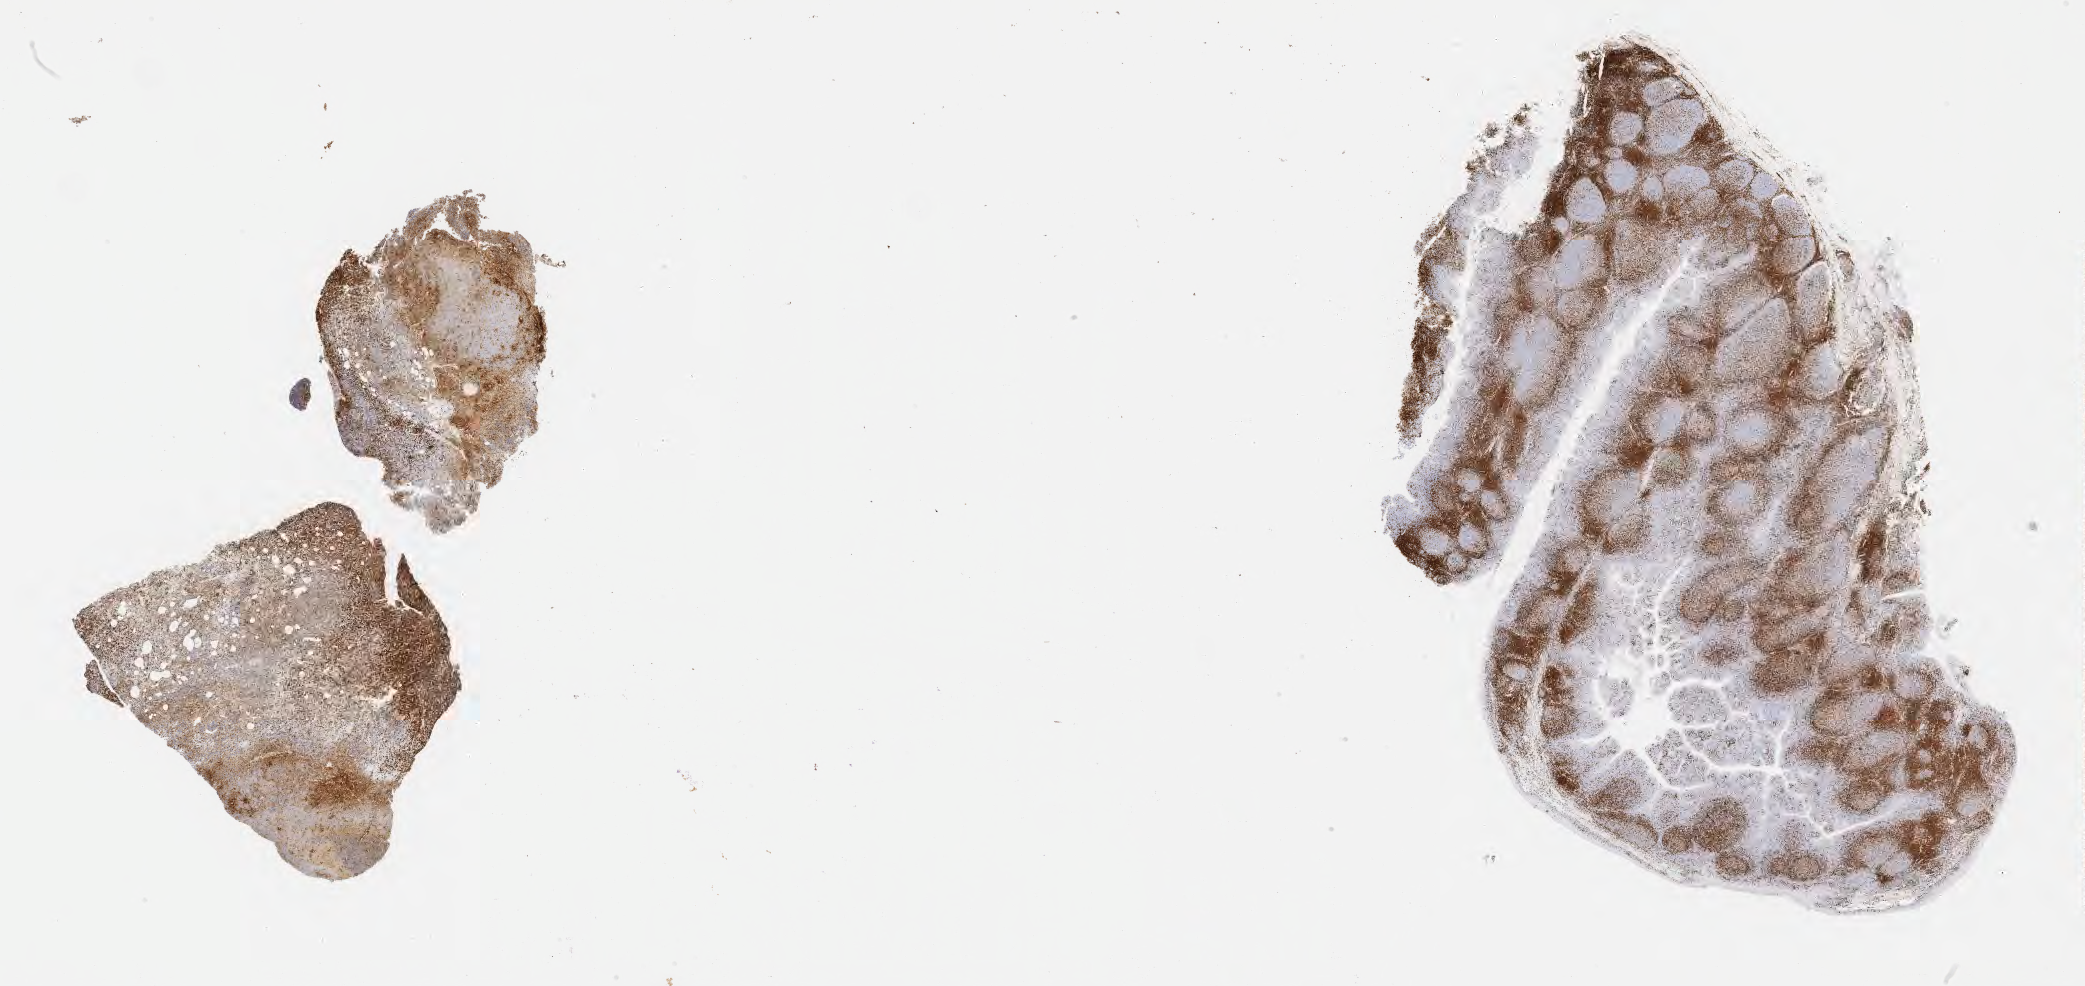
Immunohistochemistry (IHC) whole-slide image stained for CD3 — low-resolution overview of the scanned area, about 33.7 x 15.9 mm. Tumor tissue. Site: mandible. Male patient; age at initial diagnosis 7 years.
• histologic diagnosis: Burkitt lymphoma, NOS